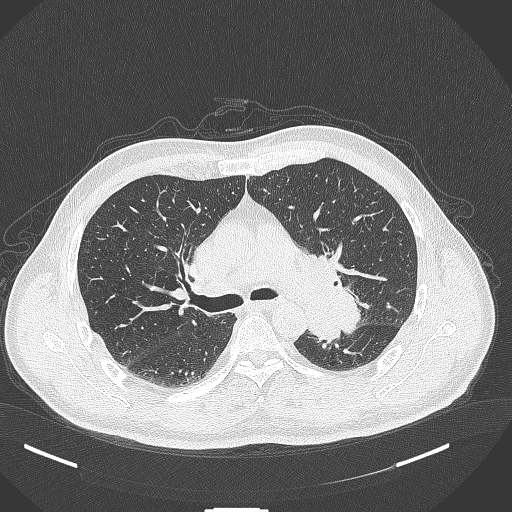
Chest CT, one axial slice. Position 262 of 429 along the scan axis. Reconstruction kernel B70f. Lung window (W 1500 / L -600 HU). 1 mm slice thickness. 512 × 512 image matrix, field of view 400 × 400 mm. Male patient, age 55 years. From the clinical record (not read from this slice): clinical TNM (as recorded): T3 N0 M1c; histopathological grade: G3.
Annotated regions visible in this slice (bounding box drawn by a radiologist):
- lung tumour (recorded histology: adenocarcinoma): bounding box (x1, y1, x2, y2) in pixels: (302, 280, 365, 344)